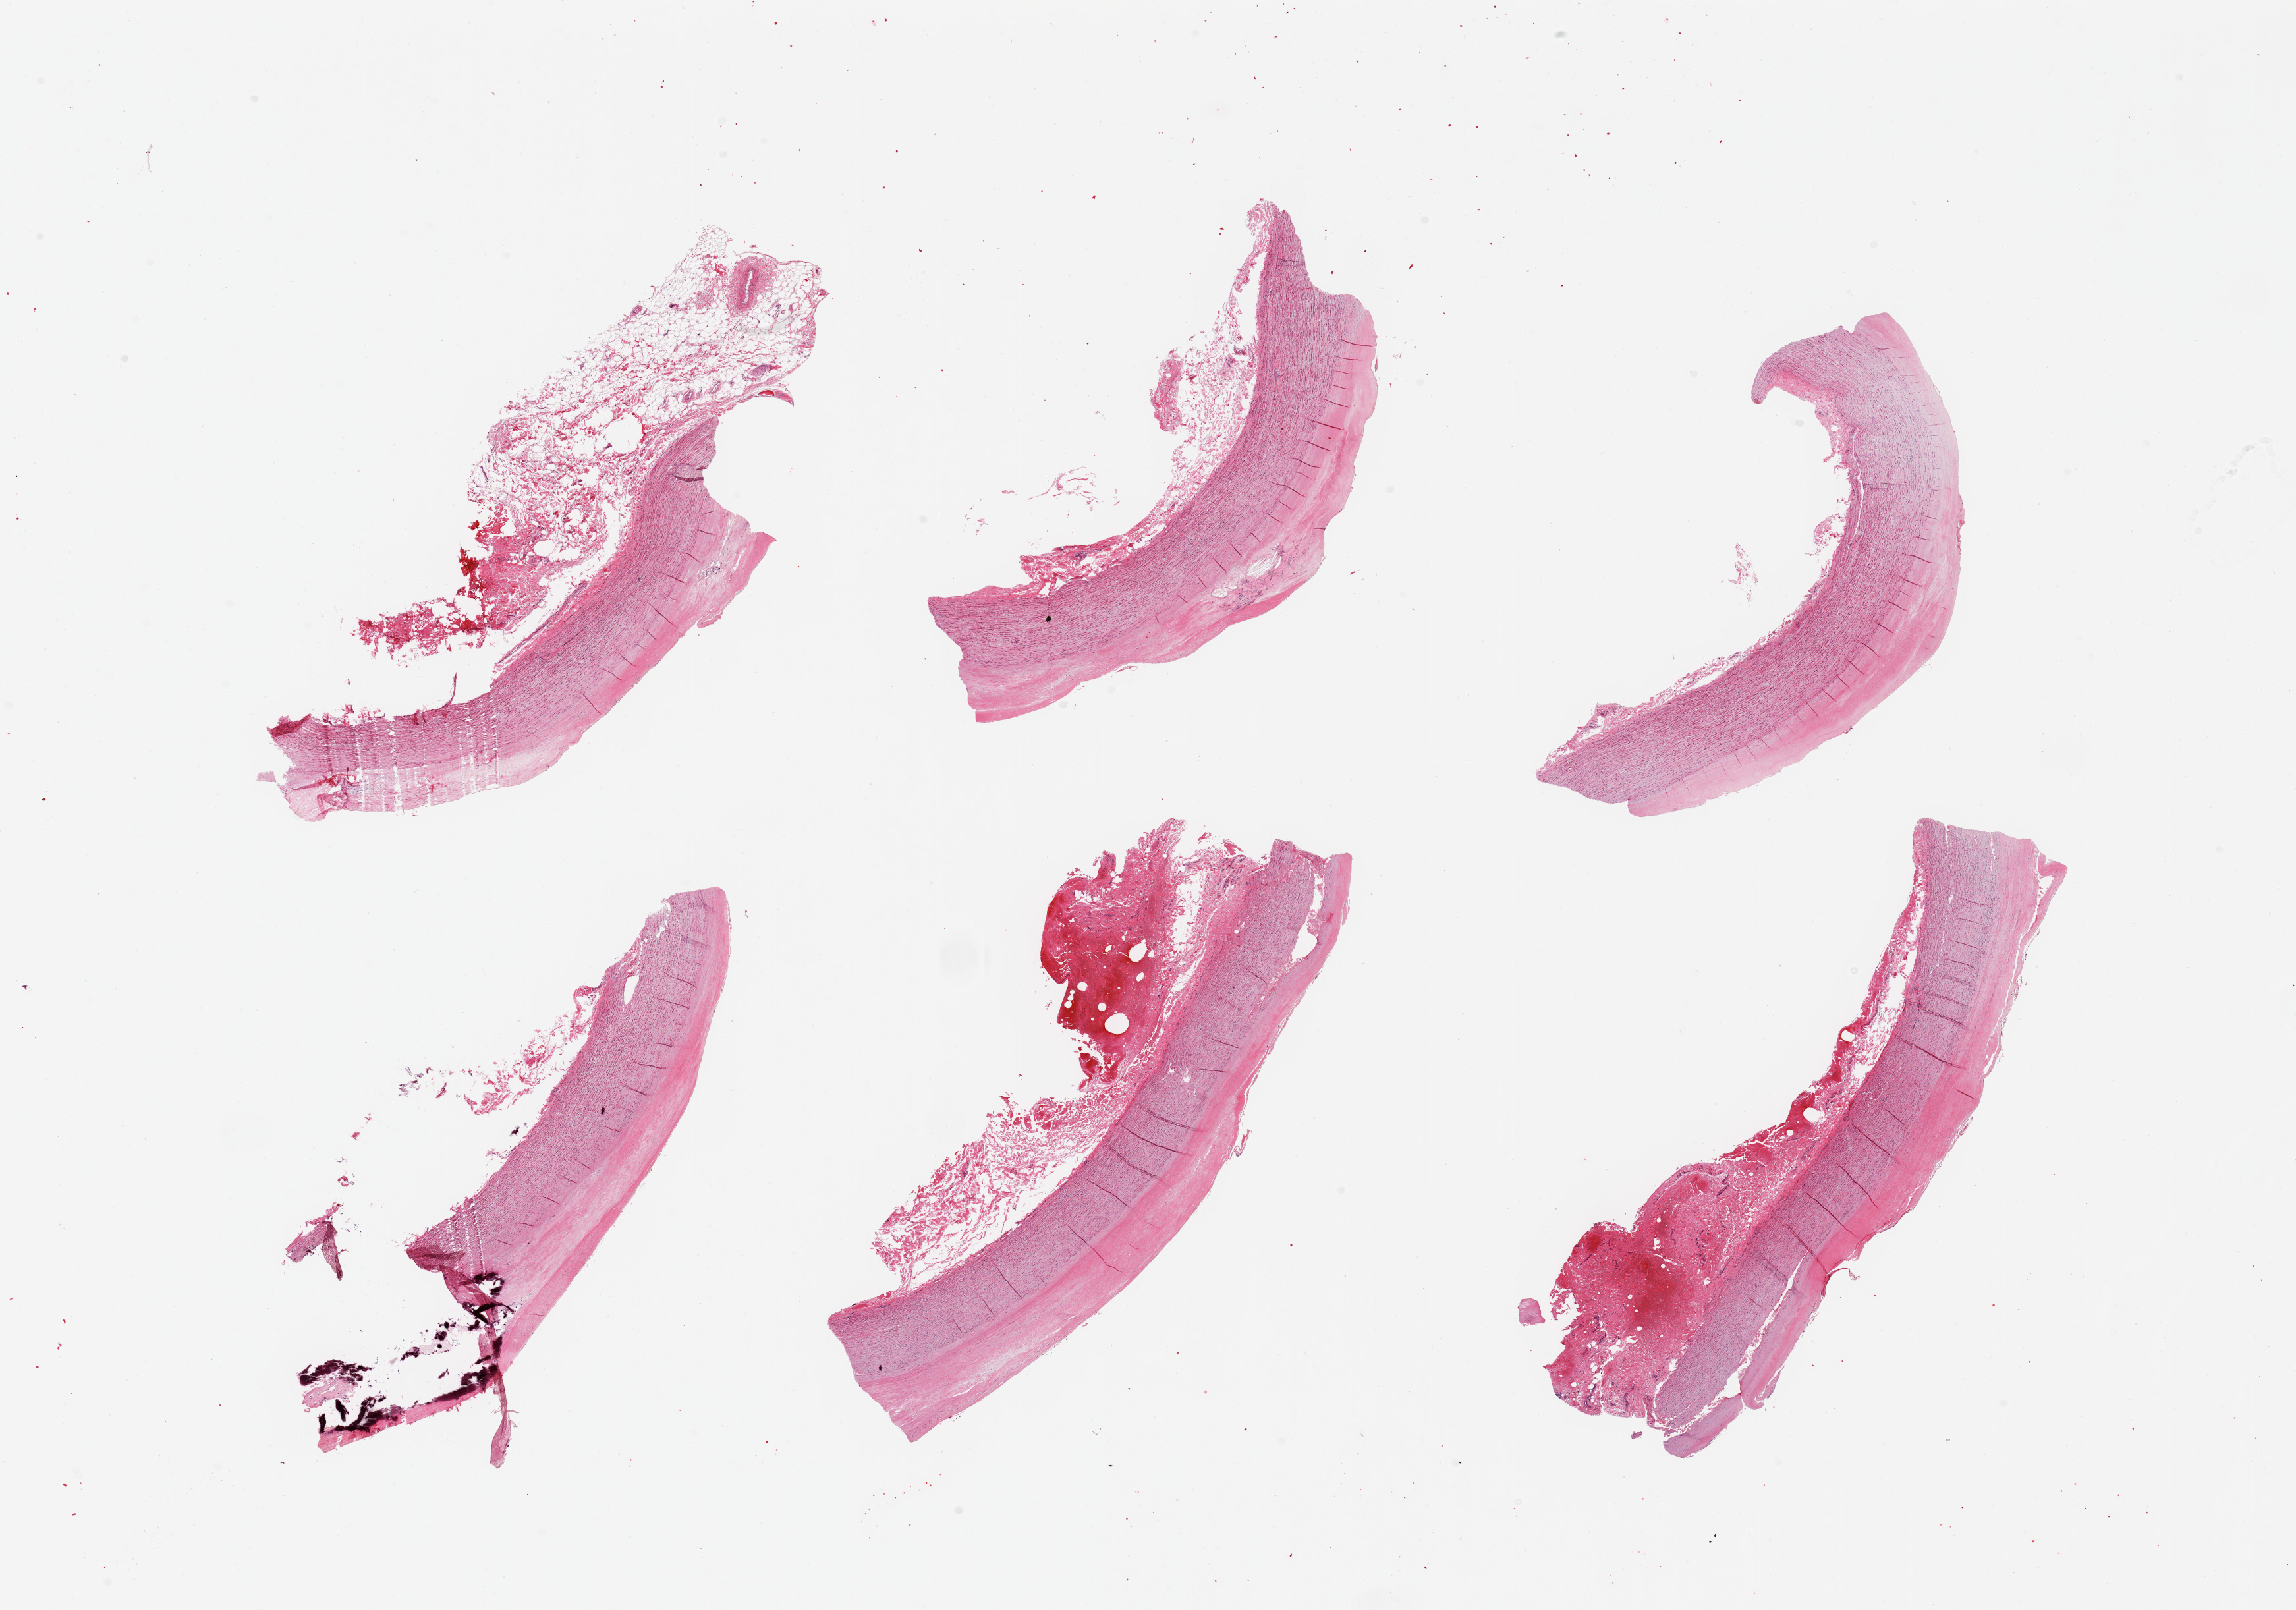
Whole-slide image, H&E stain — low-resolution overview of the scanned area, about 27.6 x 19.3 mm, PAXgene-fixed, paraffin-embedded tissue, target tissue: aorta, donor tissue sample. Donor: male.
Review note (as recorded): 6 pieces, atherosis up to ~1mm, focally calcified adherent hemorrhagic fat/serosa.